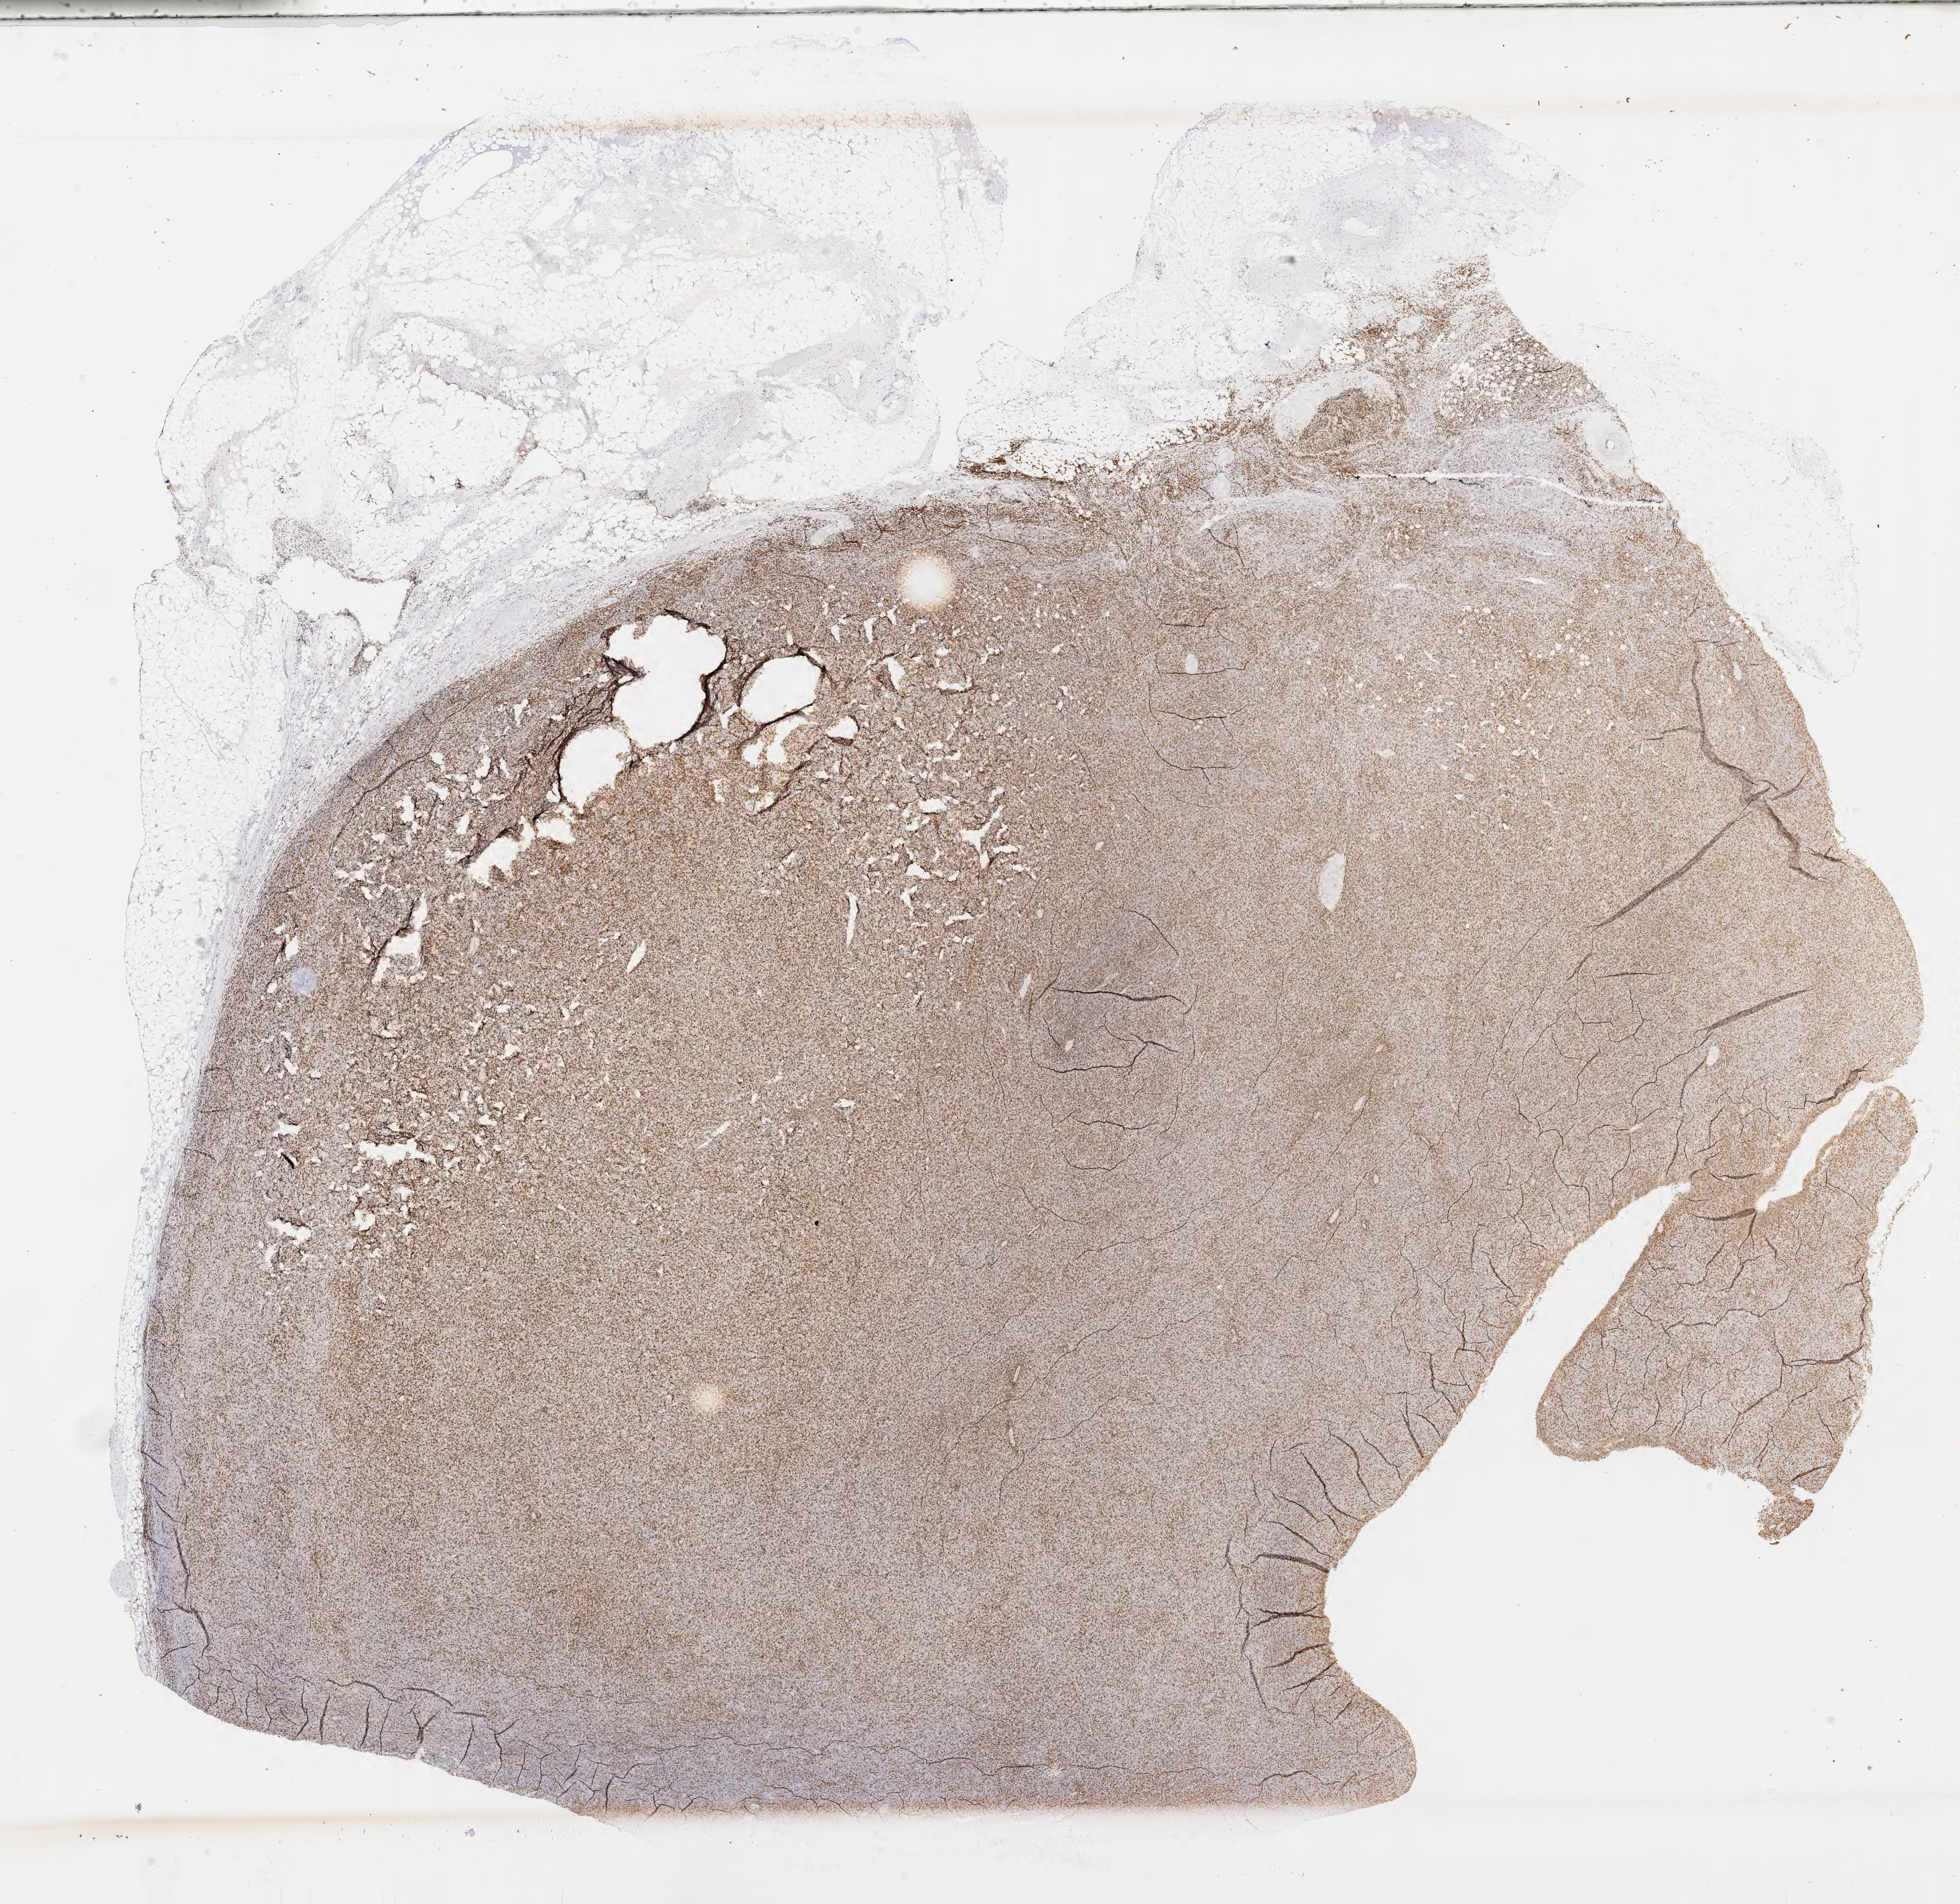
Immunohistochemistry (IHC) whole-slide image stained for CD3 — low-resolution overview of the scanned area, about 23.6 x 23.0 mm. Specimen: tumor tissue. Anatomic site: lymph node. Patient: male, aged 54.
Diagnosis: Diffuse large B-cell lymphoma, NOS.